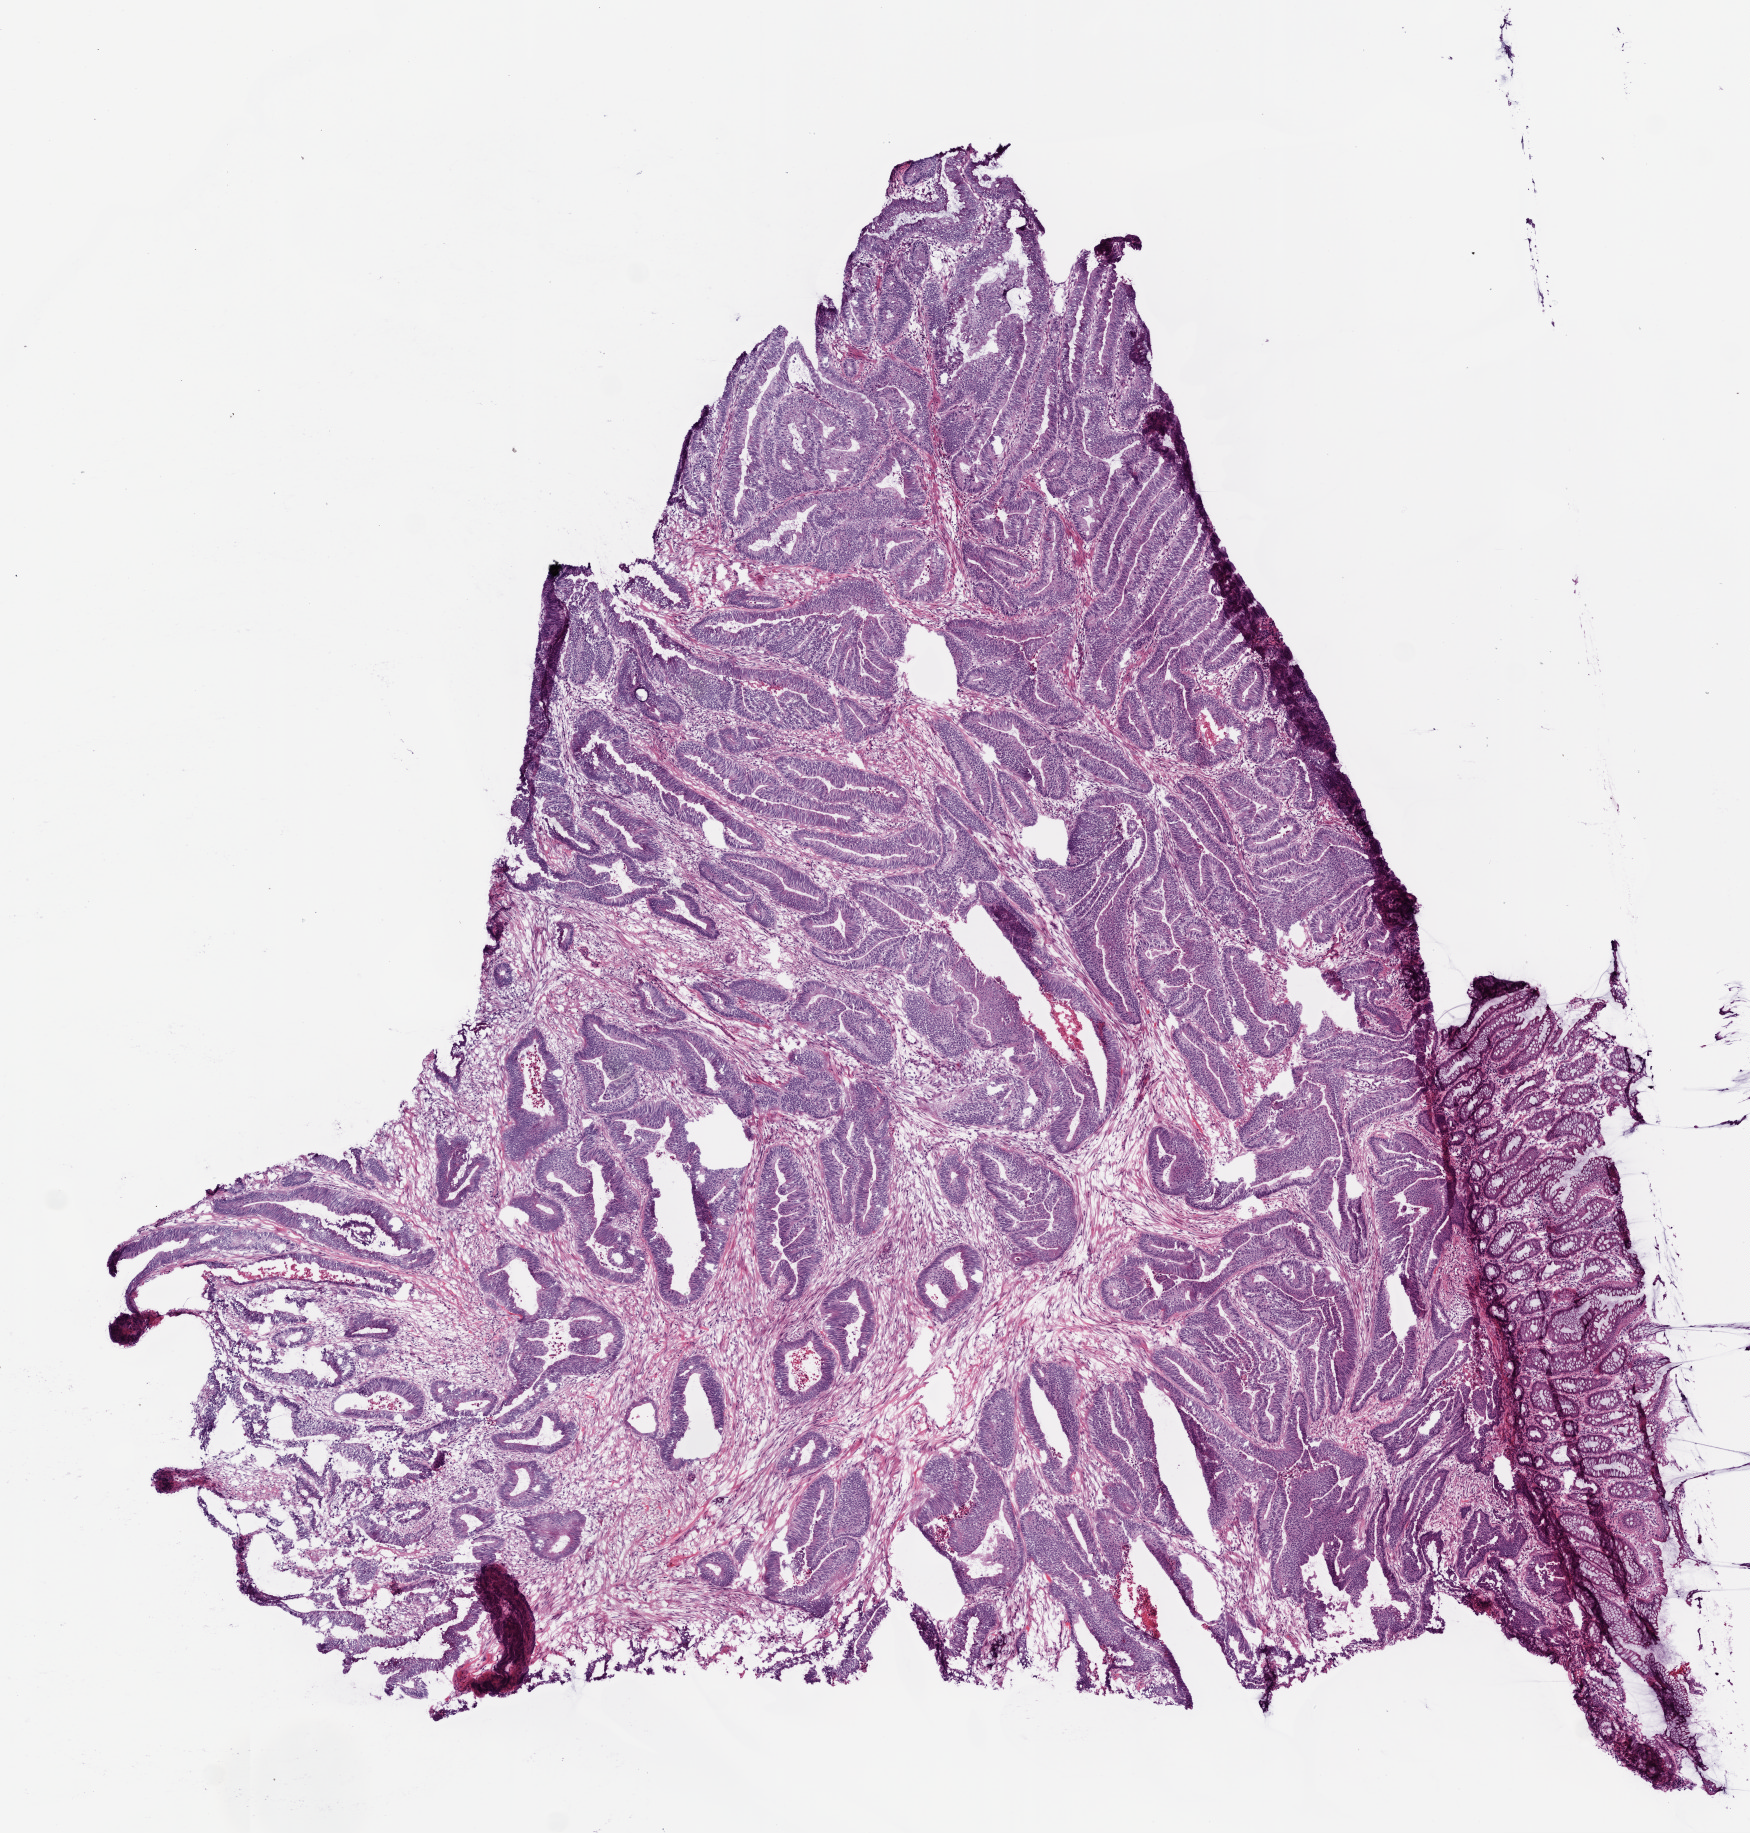
Whole-slide histology image, Hematoxylin and eosin (H&E) stained, whole scanned area (about 7.0 x 7.4 mm, slide scanned at 20x) shown as a low-resolution overview; frozen section from the top of the tissue portion; colon, primary tumour sample. Female, age 75 years at initial diagnosis. Composition of this section per pathologist review: tumour cells 72%, tumour nuclei 80%, normal cells 8%, stromal cells 15%, necrosis 5%.
* lymph nodes positive (case pathology): 1 of 26 examined
* AJCC pathologic stage: IV (6th edition)
* histologic diagnosis: Adenocarcinoma, NOS (sigmoid colon)
* TNM: T3 N1 M1